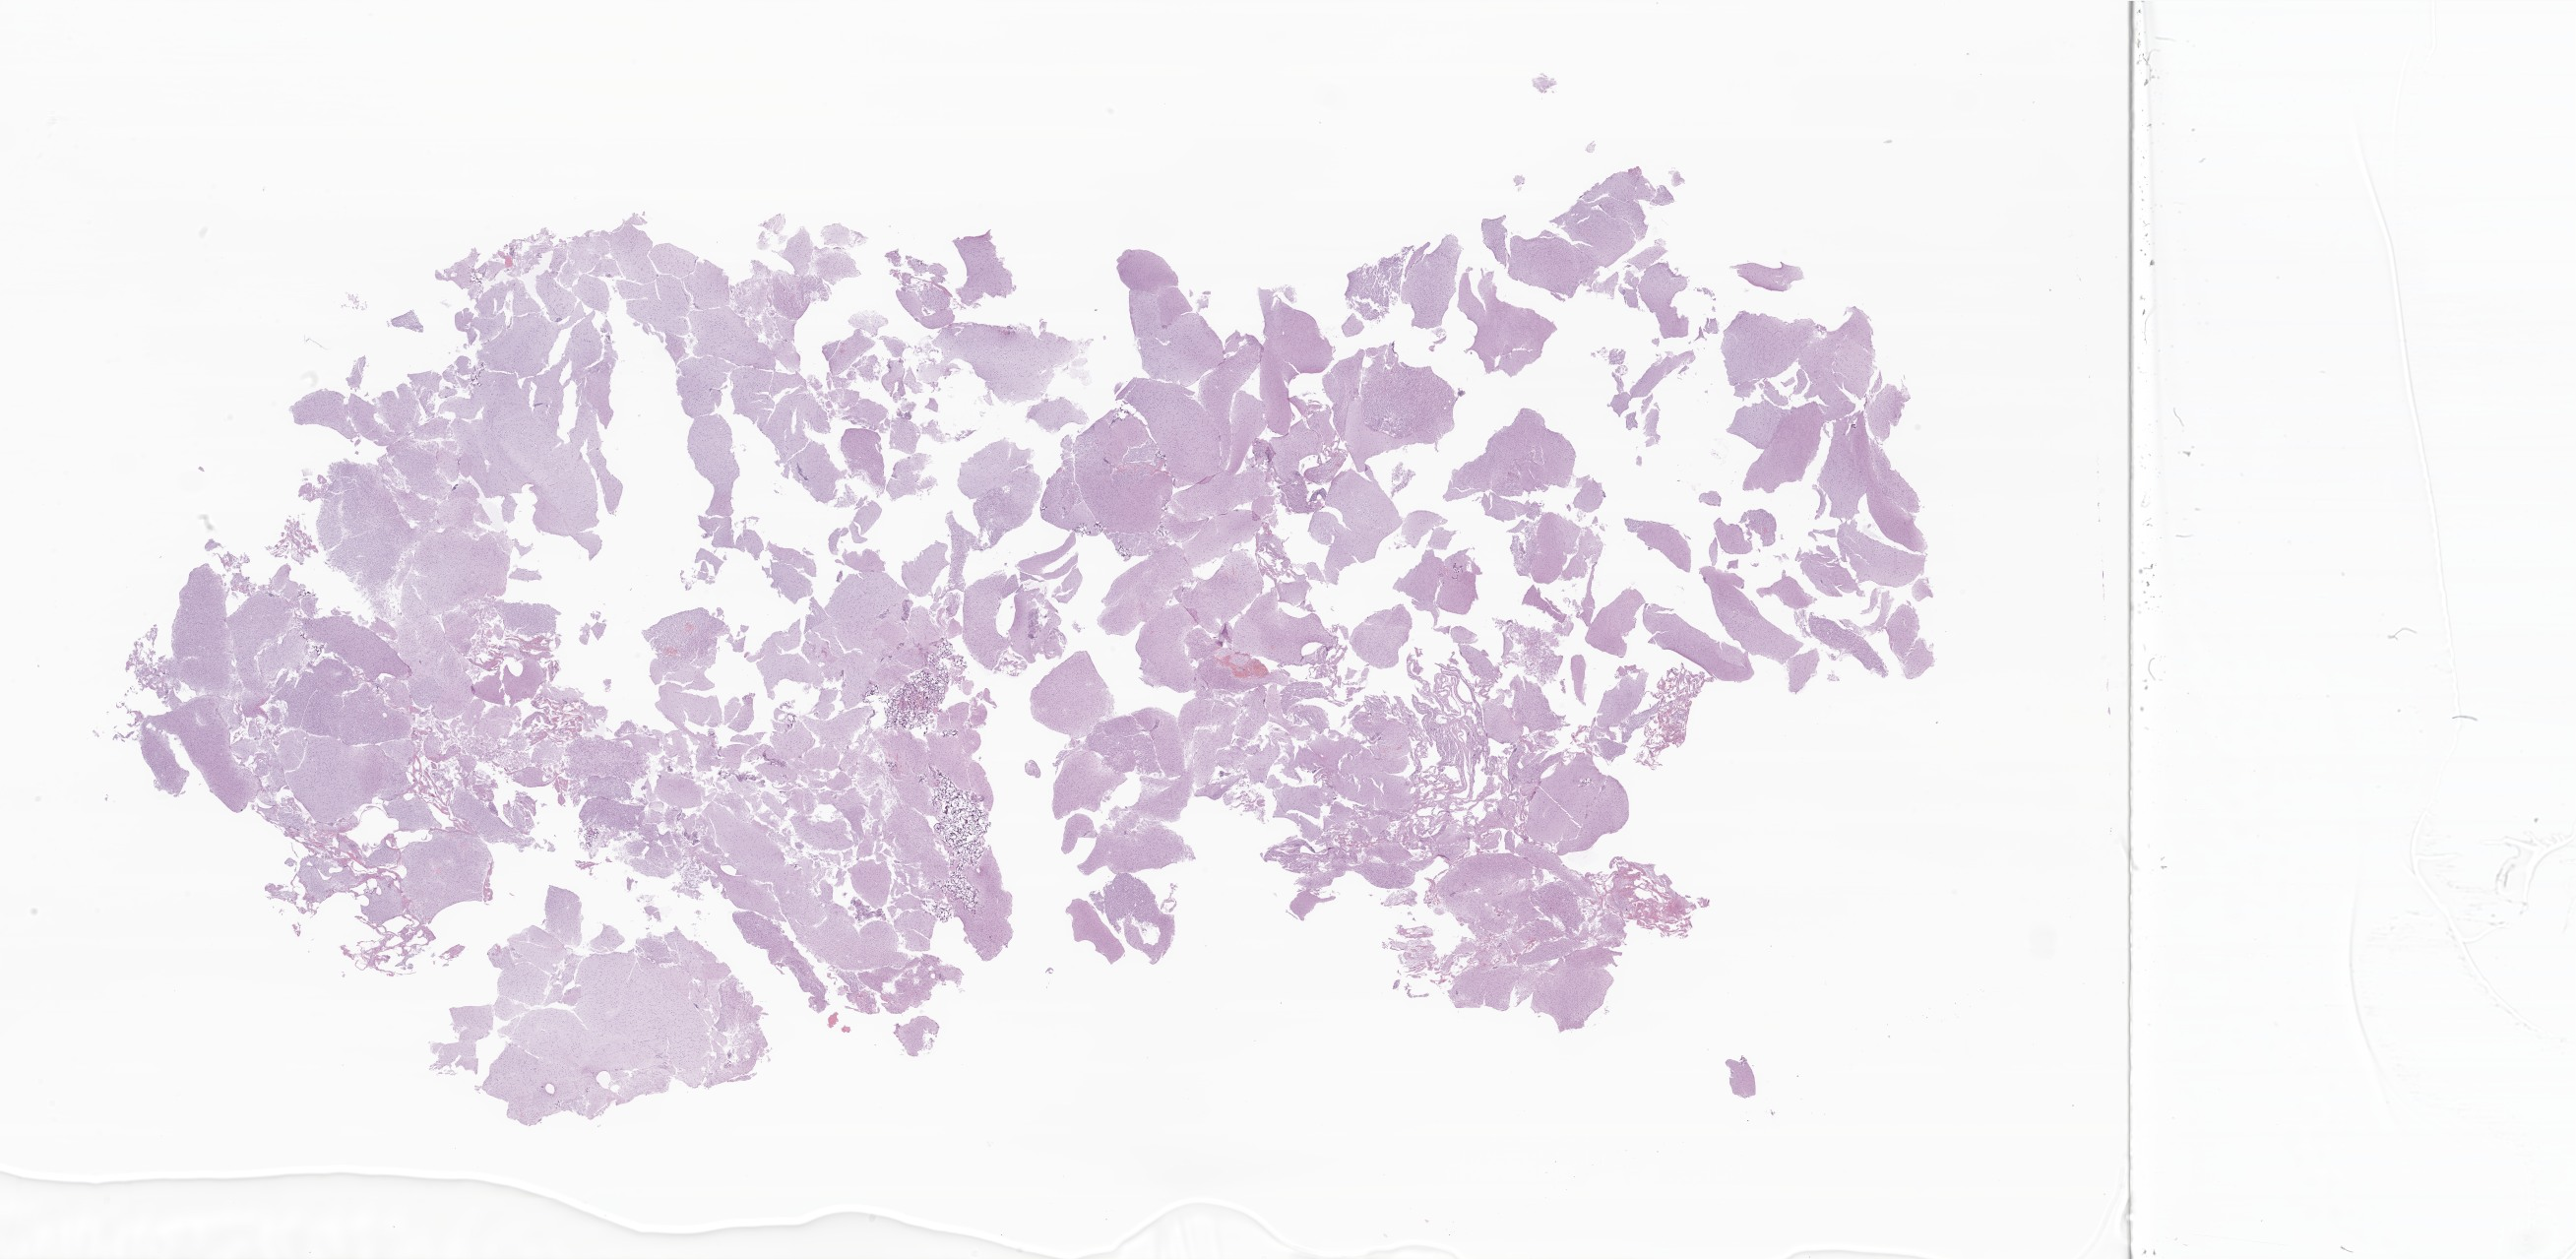
Hematoxylin and eosin (H&E) whole-slide image of tumor tissue from the brain, whole scanned area (about 44.1 x 21.6 mm) shown as a low-resolution overview. FFPE section. Male patient, age 88 months (7 years 4 months).
Diagnosis: Neoplasm, uncertain whether benign or malignant.